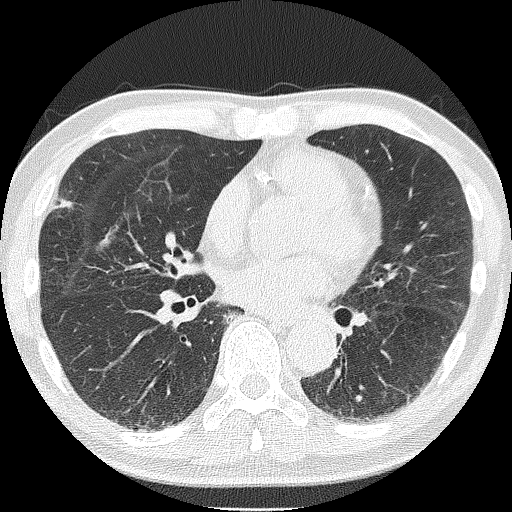
Chest CT (low-dose screening protocol), one axial image. Second screening round (one year after baseline). Lung window (W 1500 / L -600 HU). 512 × 512 image matrix, field of view 287 × 287 mm. Male participant, aged 68 years at enrolment. Current smoker at enrolment.
Expert reader's lesion annotation, bounding box (x1, y1, x2, y2) in pixels: (40, 185, 86, 226). The exam's reader record, not a measurement of the box and not confirmed to be the same lesion: non-calcified nodule or mass ≥4 mm, right upper lobe, 6 × 4 mm, spiculated (stellate) margins, soft tissue attenuation, pre-existing on the prior screen: no.